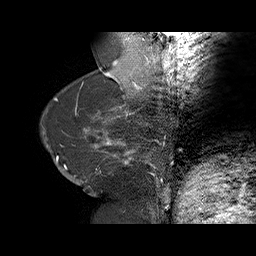
Breast MRI (dynamic contrast-enhanced), one sagittal slice; dynamic contrast-enhanced series, time point 2 of 6 at this slice position (early post-contrast); 1.5 T; TE 4.5 ms, TR 32.4 ms; 3 mm slice thickness; 256 × 256 image matrix. Female patient. Case-level facts recorded for this patient, not image findings: setting: breast cancer imaged before/during neoadjuvant chemotherapy; receptor status: HR-positive, HER2-negative.
Structures marked on this image (semi-automatic segmentation, software-assisted and operator-edited):
- analysis volume of interest (the breast-tissue region the enhancement analysis was run in; not a lesion): bounding box <58,134,166,191> (left, top, right, bottom; pixels)
- tumour enhancement mask (voxels above the 100 % enhancement threshold inside the analysis volume of interest): <94,137,160,187>